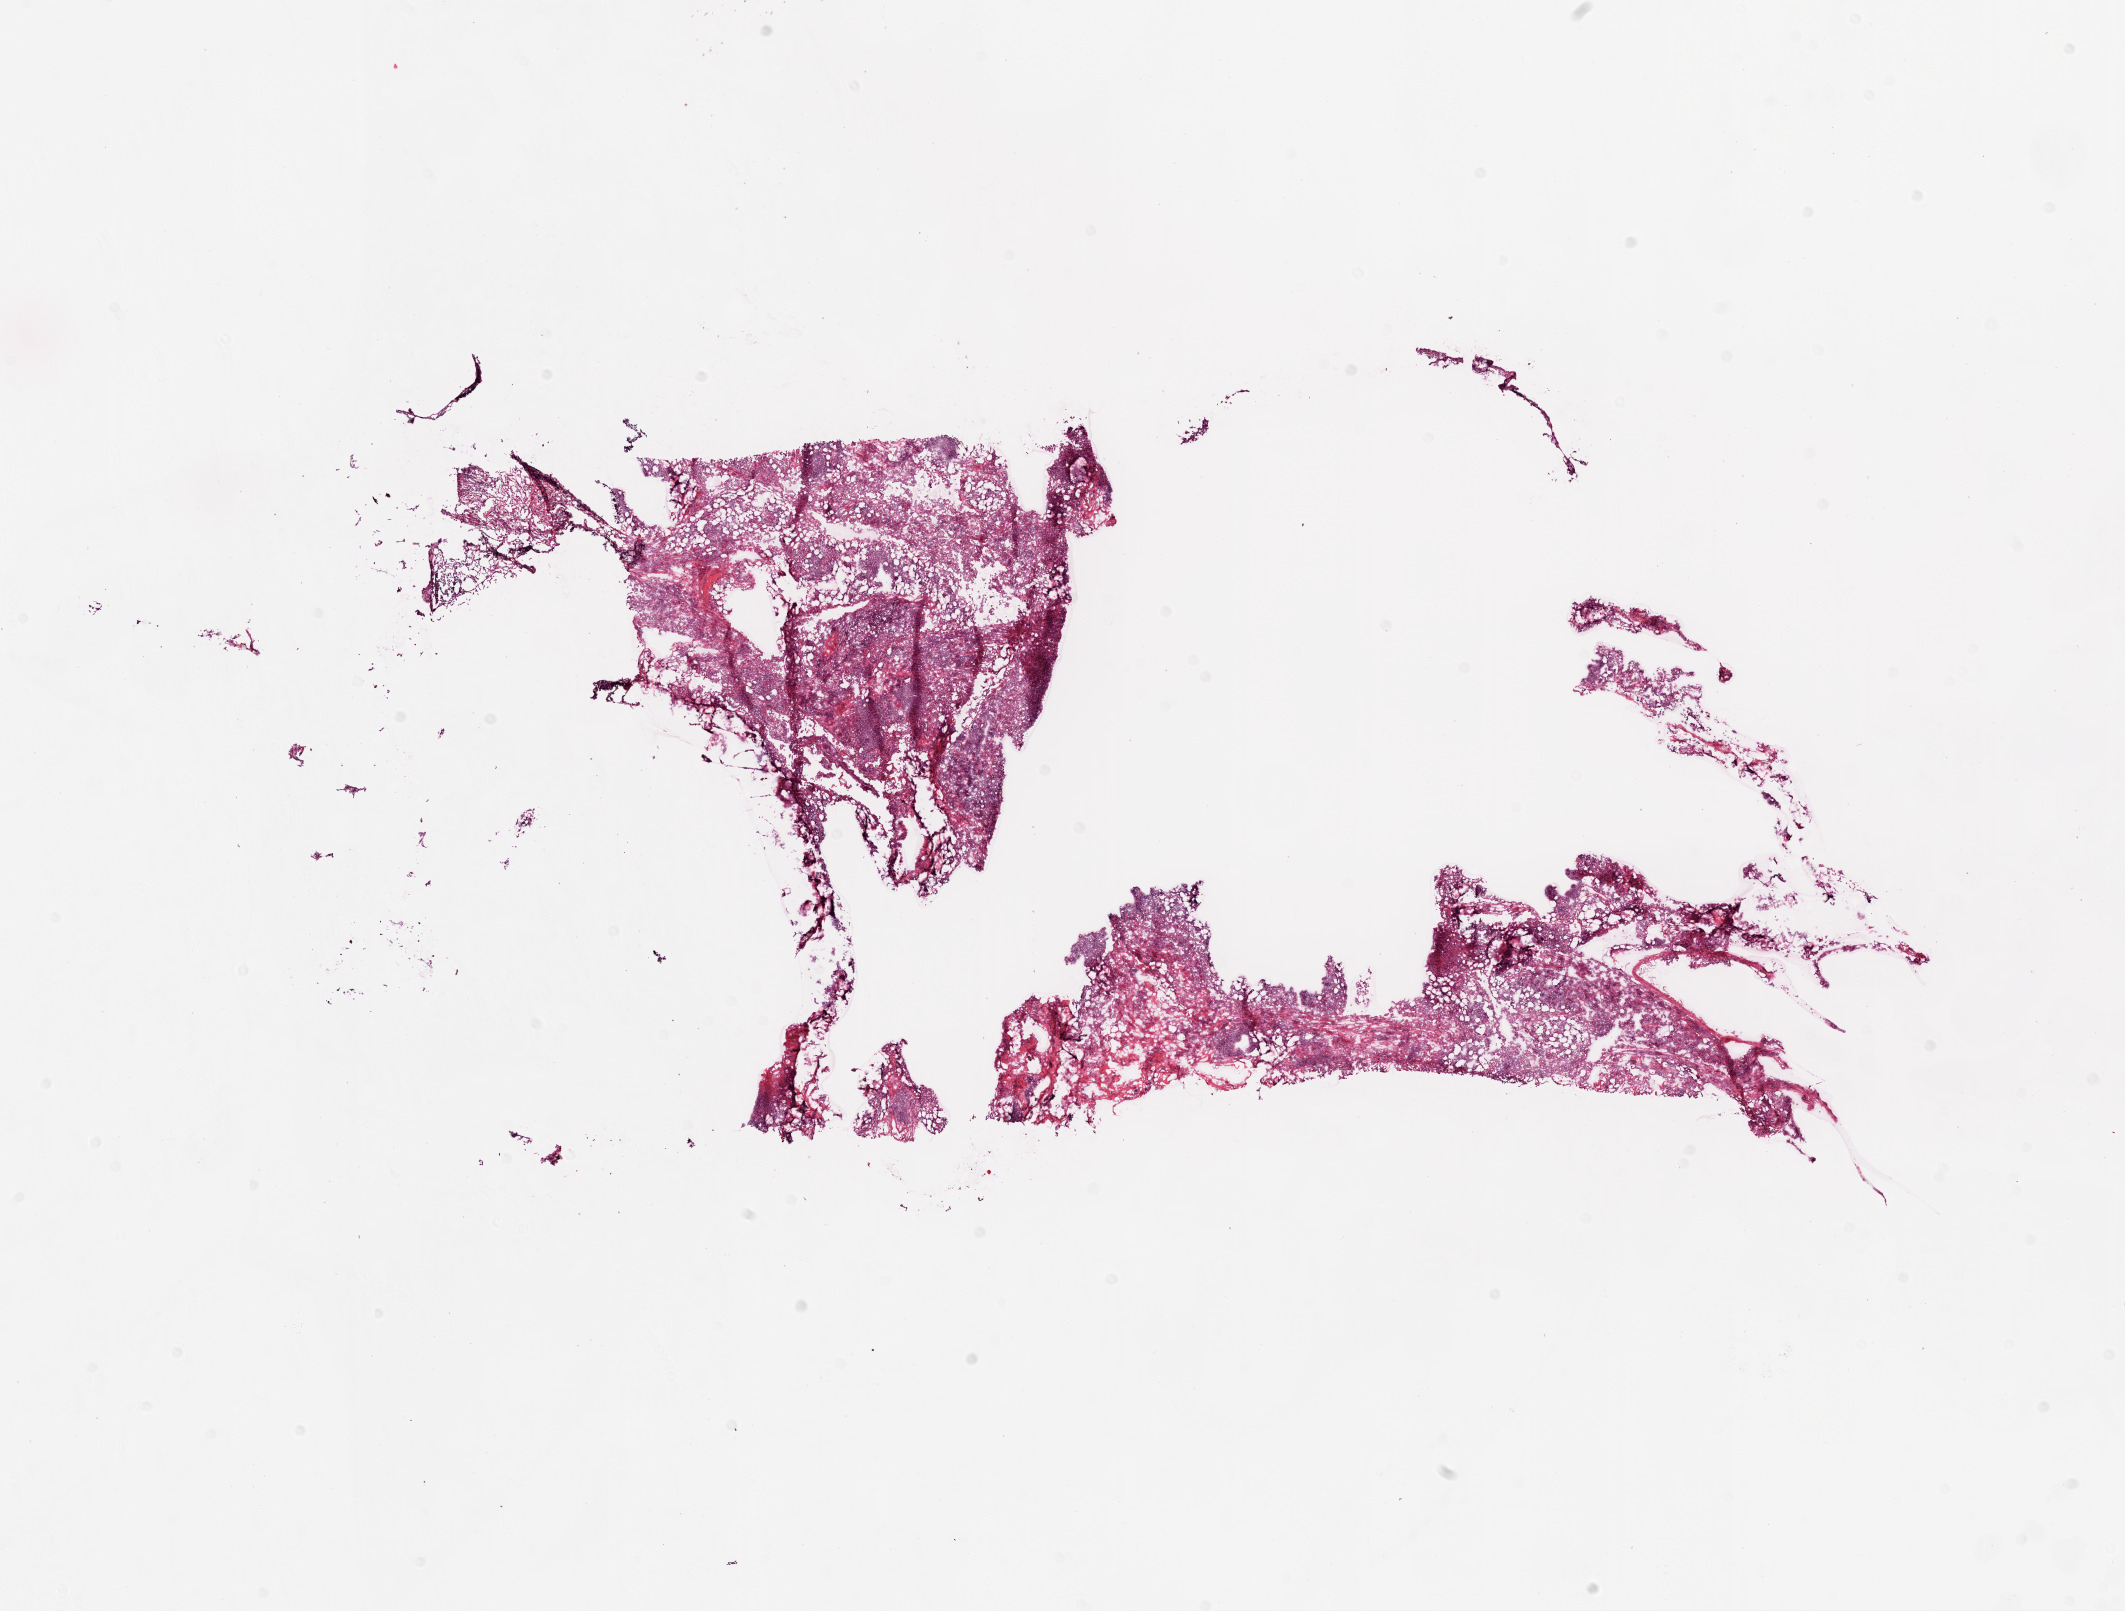
Digitized H&E tissue section (whole slide), low-resolution overview of the scanned area, about 17.1 x 12.9 mm (acquisition: 20x scan), frozen section, sample: solid tissue normal (non-tumour tissue), ovary. Female, age 57 years at initial diagnosis.
This section: solid tissue normal (non-tumour) sample from the same patient. Patient diagnosis: Serous cystadenocarcinoma, NOS.